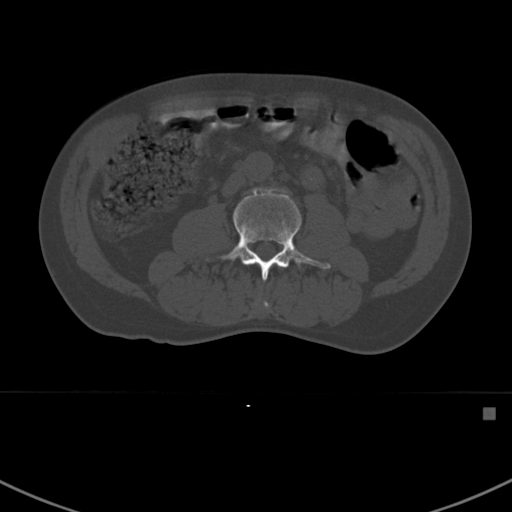
CT including the spine, one axial slice; position 264 of 412 along the scan axis; 120 kVp; bone window (W 1800 / L 400 HU); 1.5 mm slice thickness; 512 × 512 image matrix. Patient: male, 59 years. Case-level facts recorded for this patient, not image findings: primary cancer: prostate.
Annotated regions visible in this slice (semi-automatically segmented with operator editing):
- L2 vertebra: bounding box (x1, y1, x2, y2) in pixels: (262, 301, 269, 309)
- L3 vertebra: (208, 188, 331, 281)